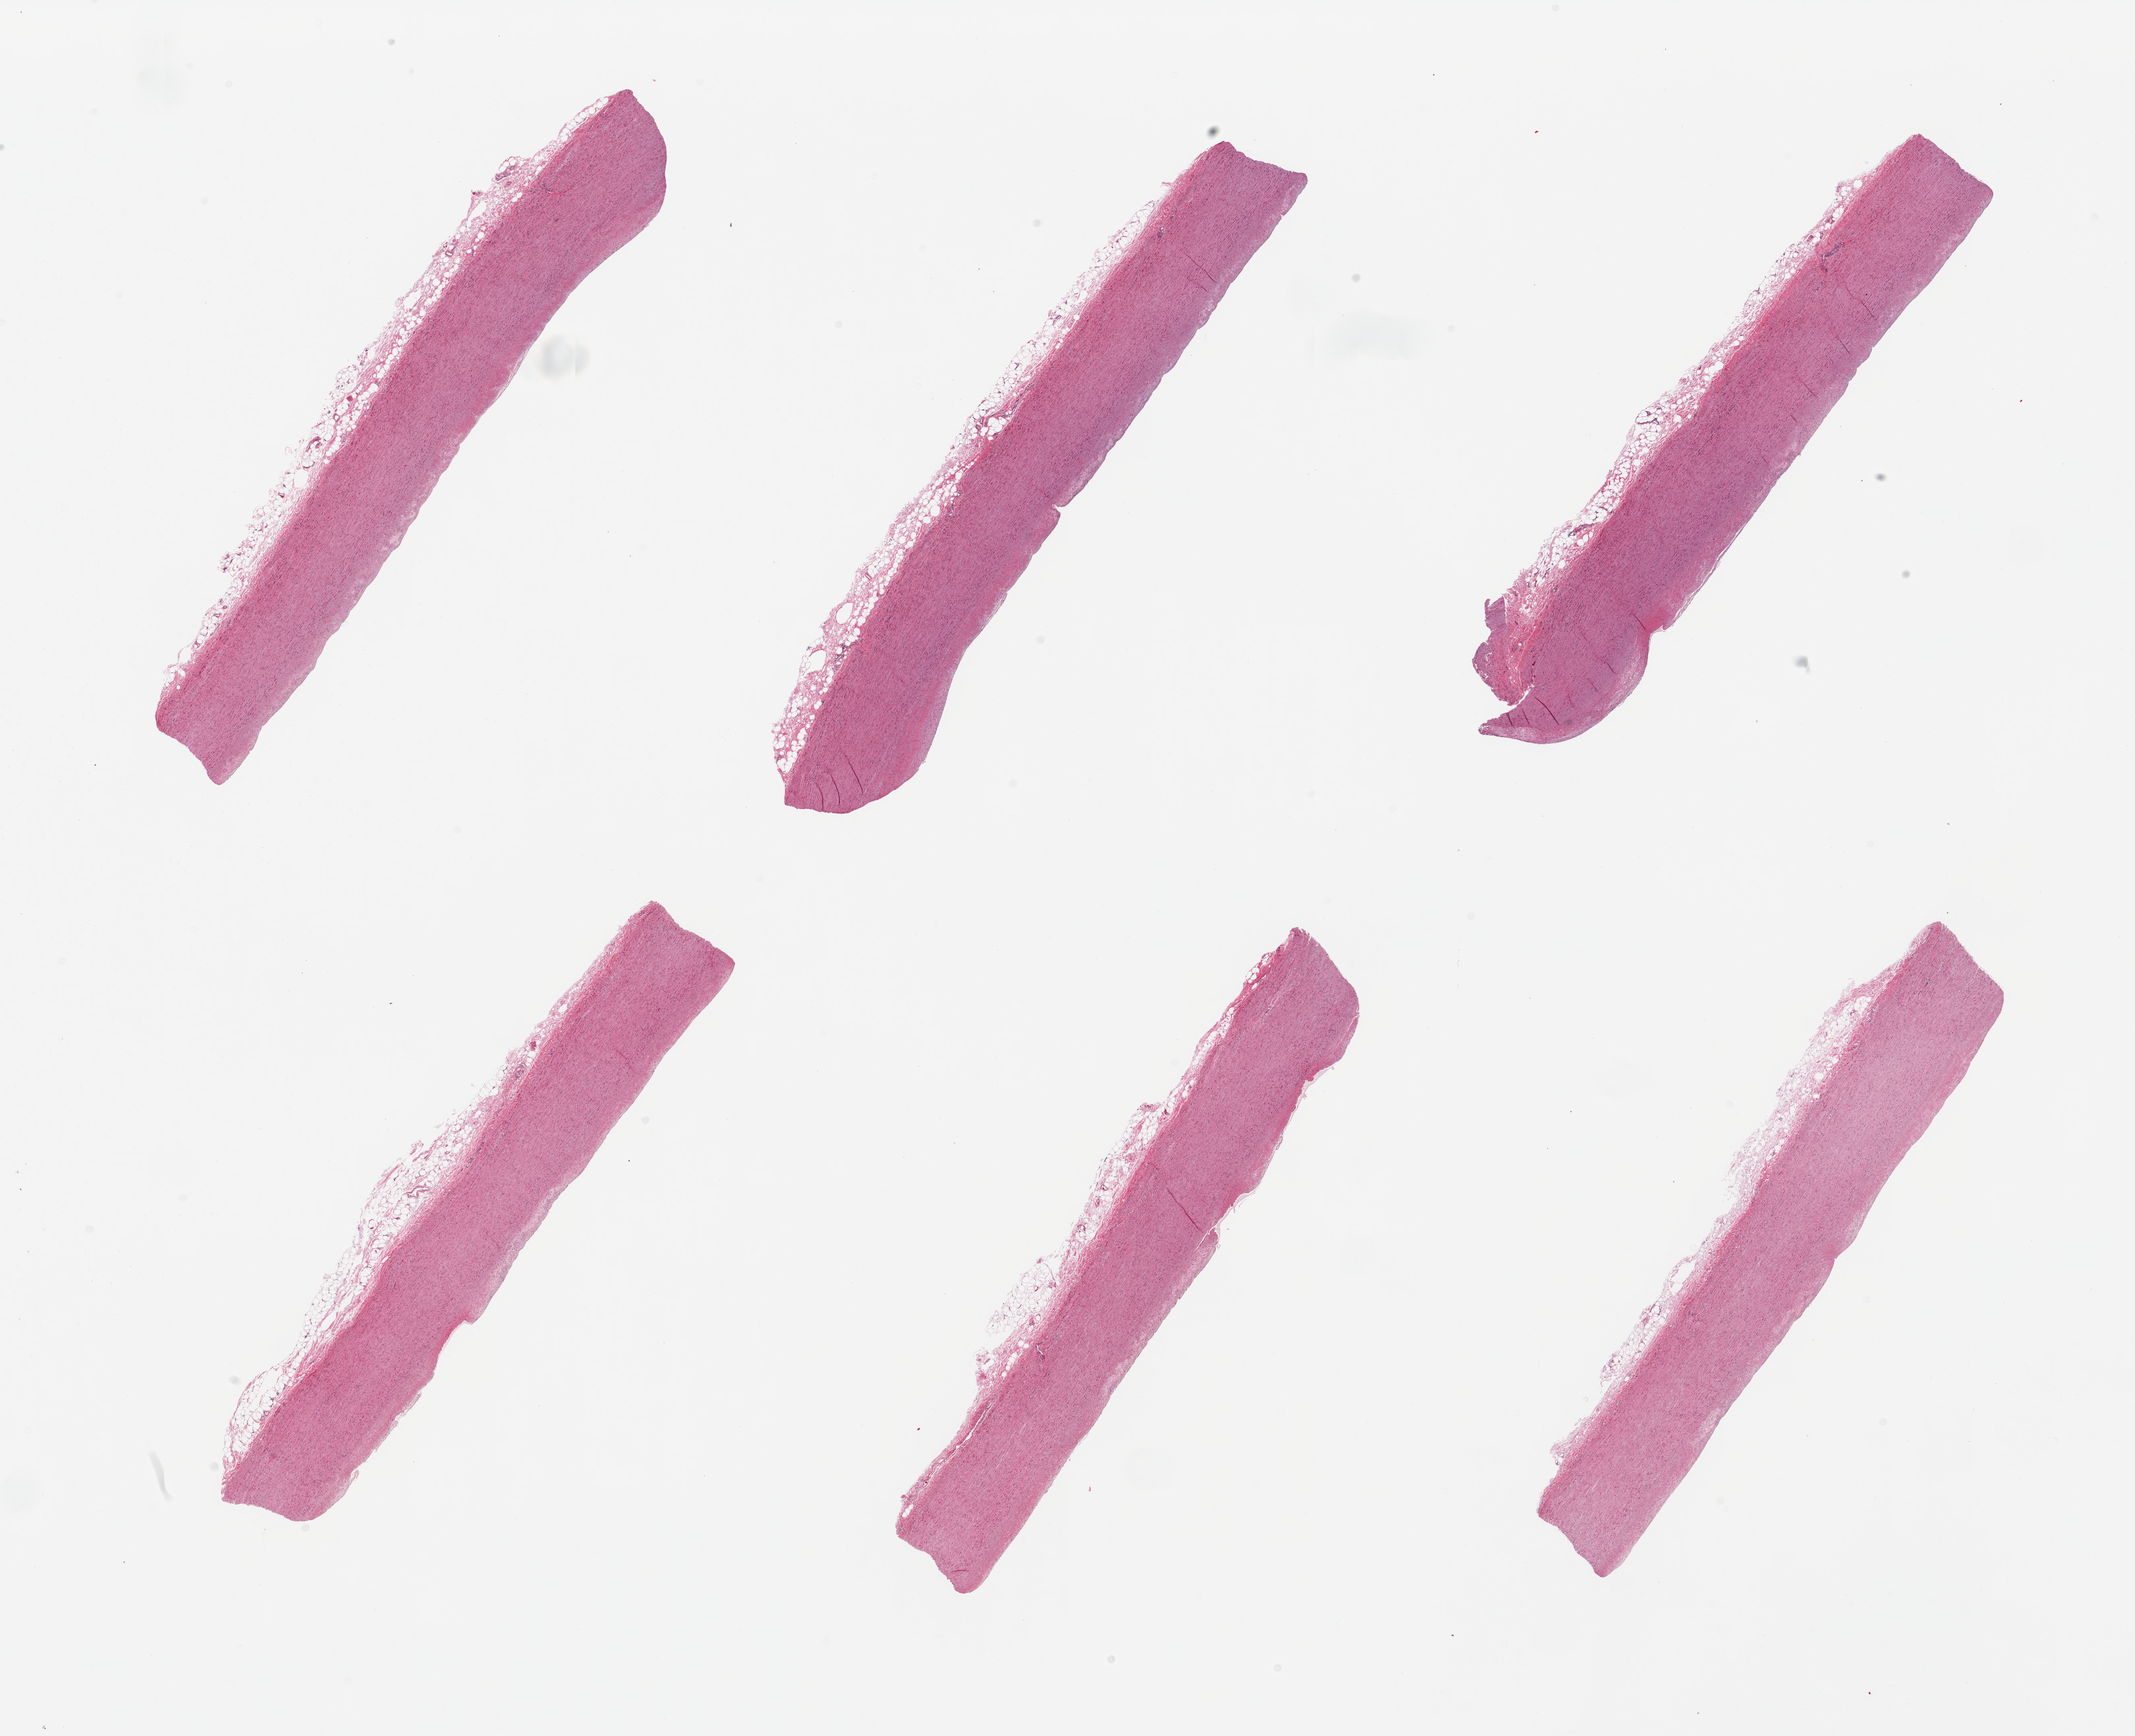
Whole-slide image, haematoxylin and eosin stain, low-resolution overview of the scanned area, about 25.6 x 20.8 mm (from a 20x scan). PAXgene-fixed, paraffin-embedded tissue. Section of aorta (target tissue). Tissue donor sample.
Pathologist's review note for this sample: 6 pieces, minimal atherosis.